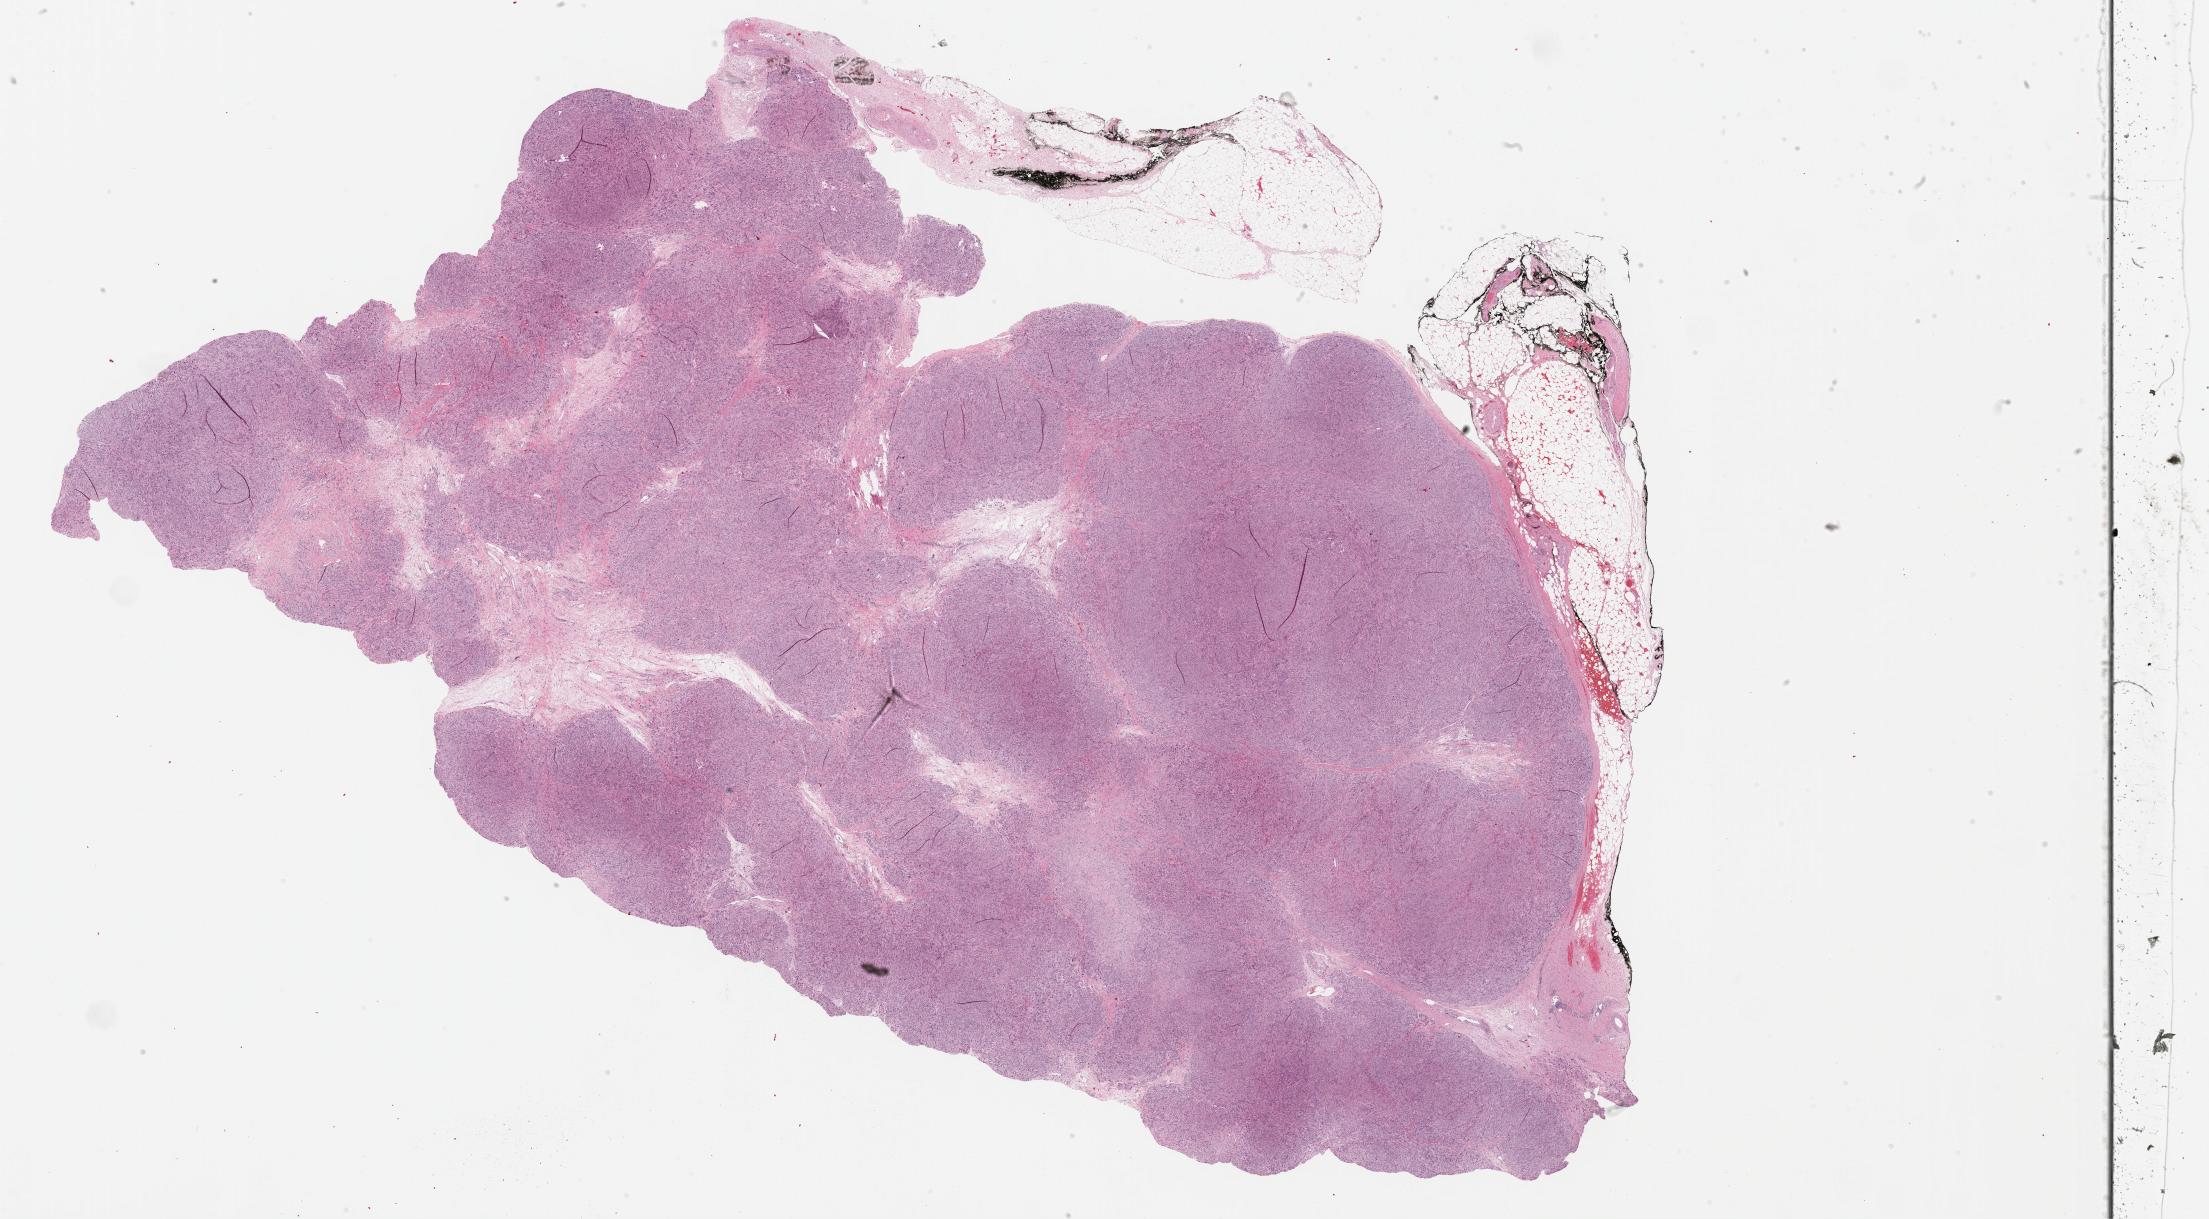
Hematoxylin and eosin (H&E) stained whole-slide image — a low-resolution overview of the entire scanned area, about 35.7 x 19.7 mm, formalin-fixed paraffin-embedded (FFPE) diagnostic section, retroperitoneum and peritoneum, primary tumour sample. Female patient; age at initial diagnosis 54 years.
• diagnosis: Leiomyosarcoma, NOS (retroperitoneum)